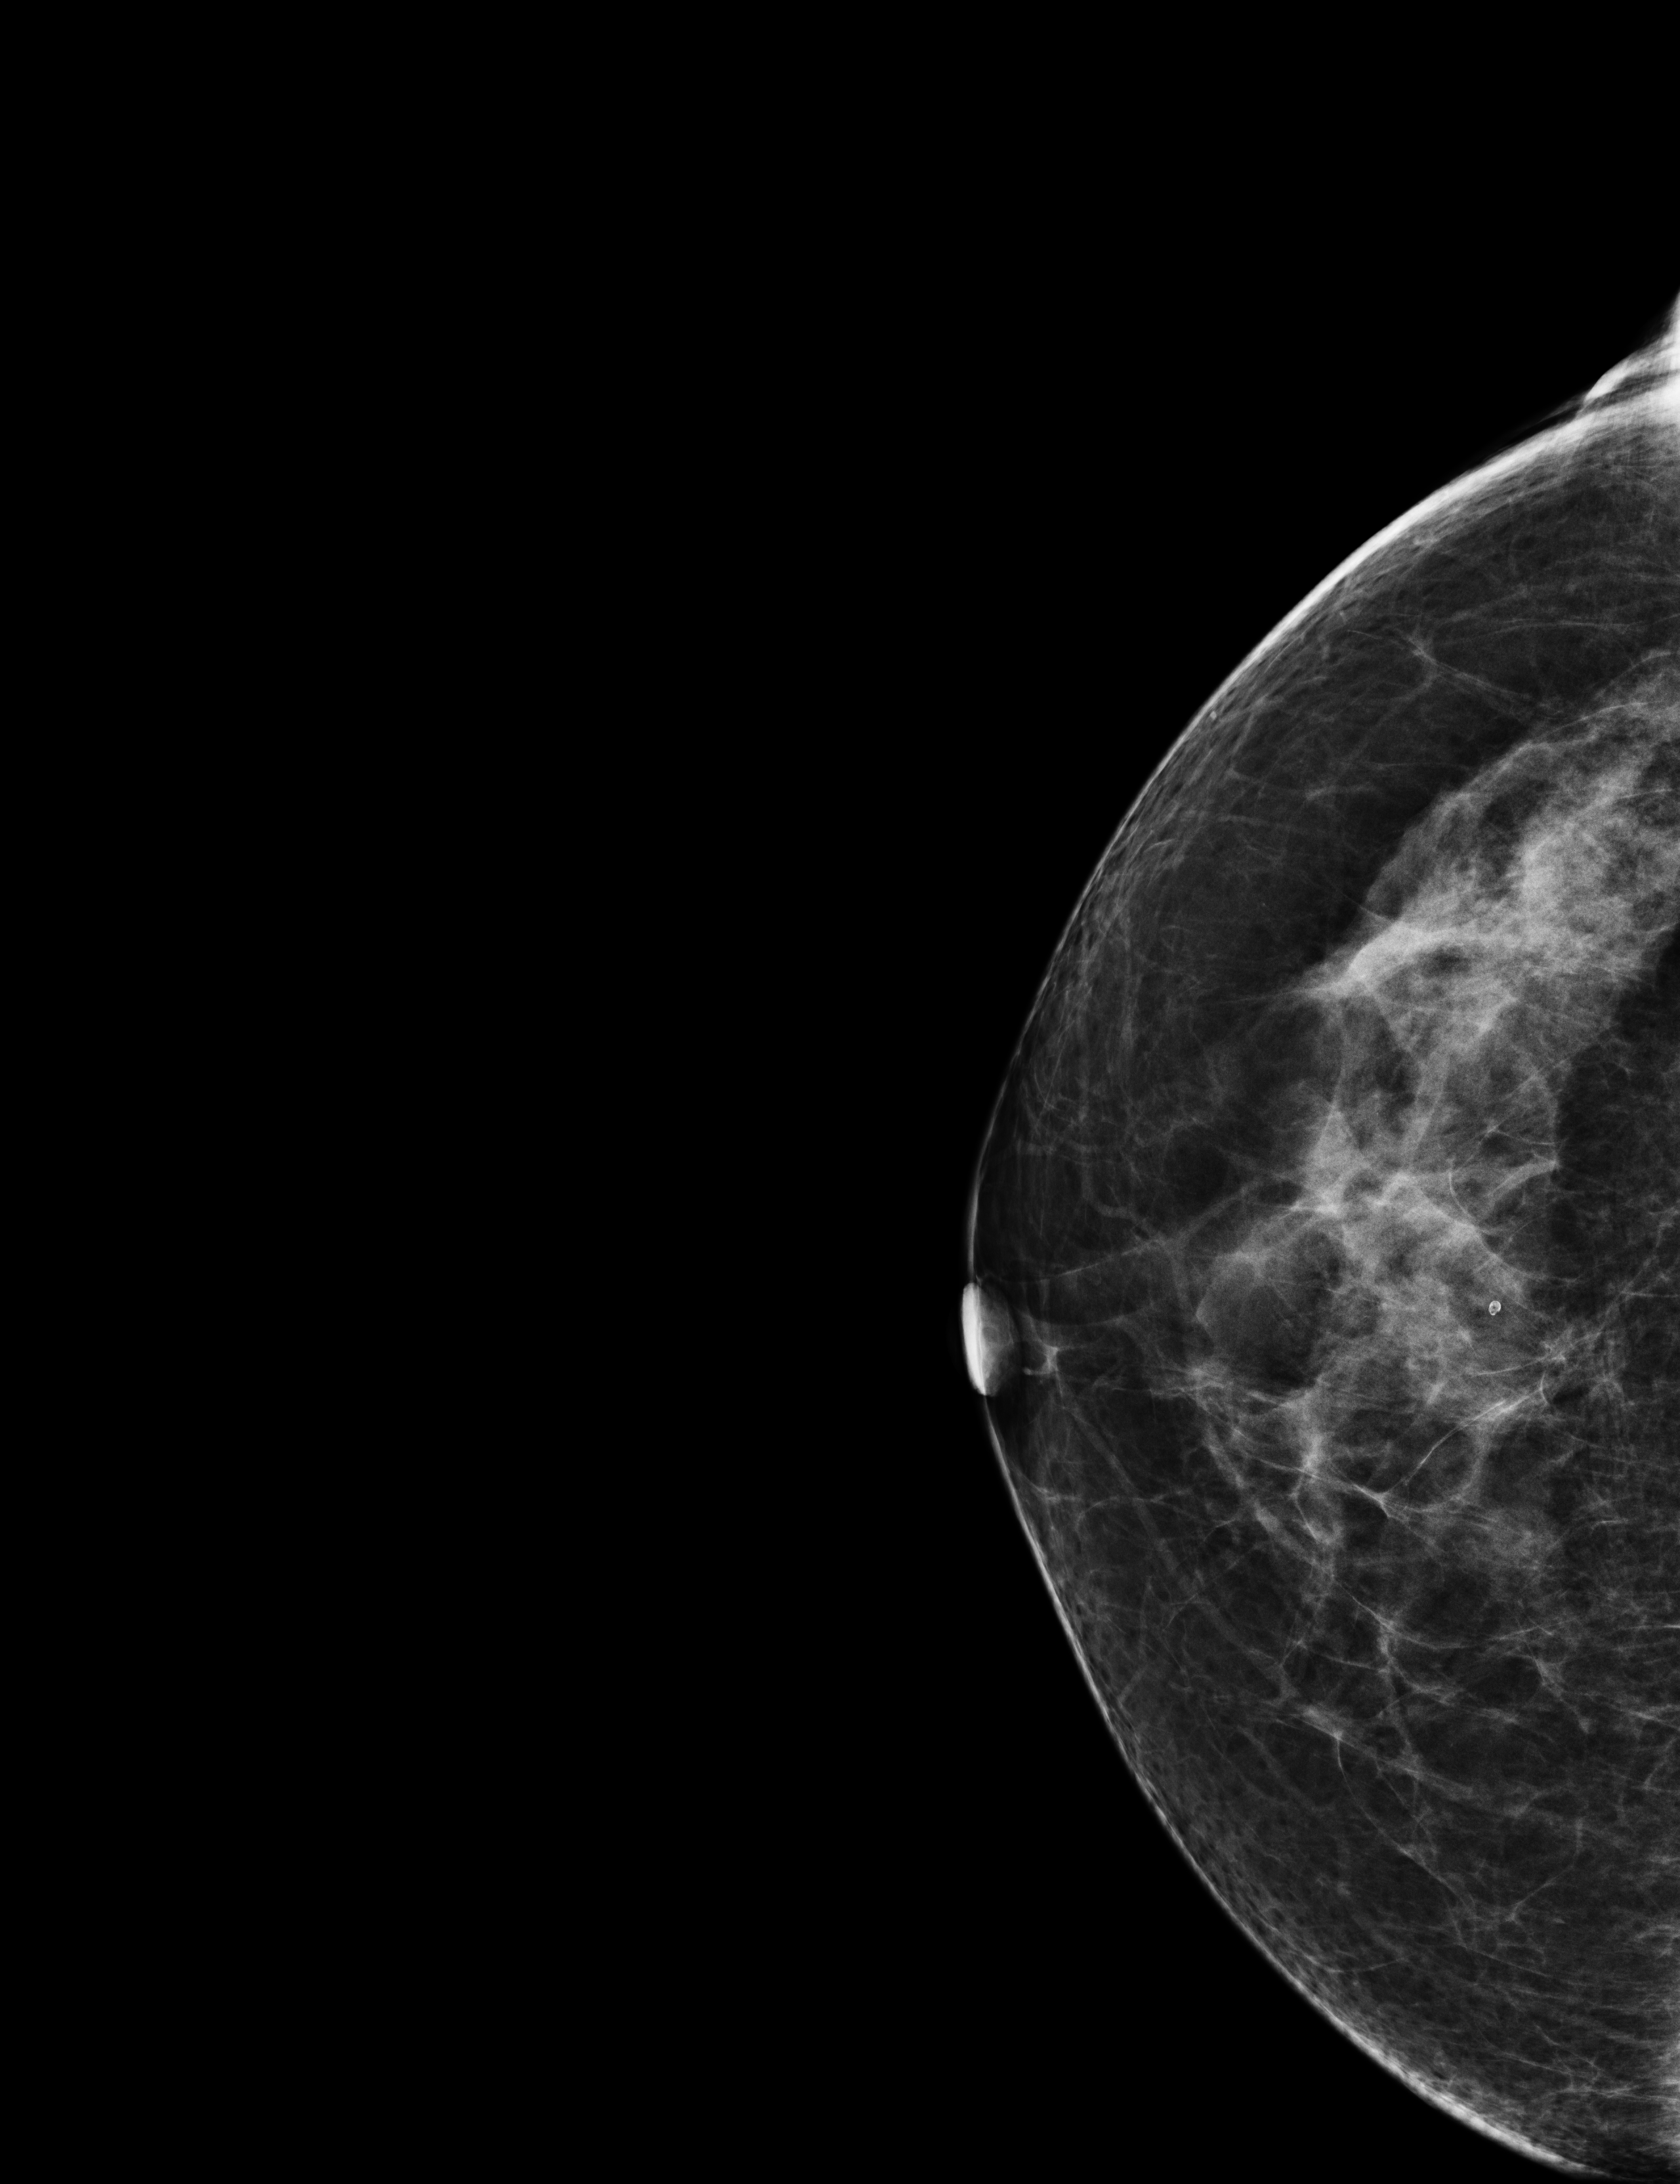
Full-field digital mammogram (FFDM), right breast, cranio-caudal projection, annual screening mammography examination. Female patient, age 63 years.
BI-RADS breast density category at the screening exam (both breasts, scale 1–4): 3. Final BI-RADS assessment for this screening round (tomosynthesis exam, both breasts): category 1. Recall: no recall after this screen.